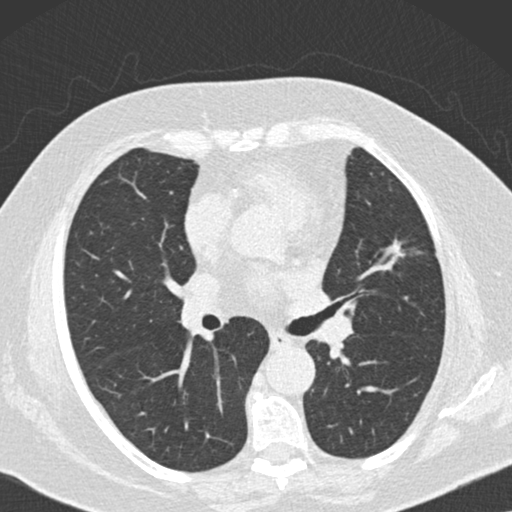
Axial slice from a low-dose chest CT screening exam, baseline screening round, lung window (W 1500 / L -600 HU). Female, age 73 years at enrolment. Current smoker at enrolment.
• Expert reader's lesion annotation, box from (x=372, y=233) to (x=417, y=275) px.
• Reader record for this screening exam (exam-level; its link to the box is not recorded): non-calcified nodule or mass ≥4 mm, right lower lobe, 7 × 7 mm, soft tissue attenuation.
• Note: the box lies in the patient's left hemithorax on this image, whereas the reader's record names the right lung; they may be different findings.
• Later outcome: lung cancer diagnosed 504 days after this screen (after the second annual screen) — adenocarcinoma, NOS, left upper lobe, moderately differentiated (G2), stage IIIB (AJCC 6th edition), 12 mm at pathology.